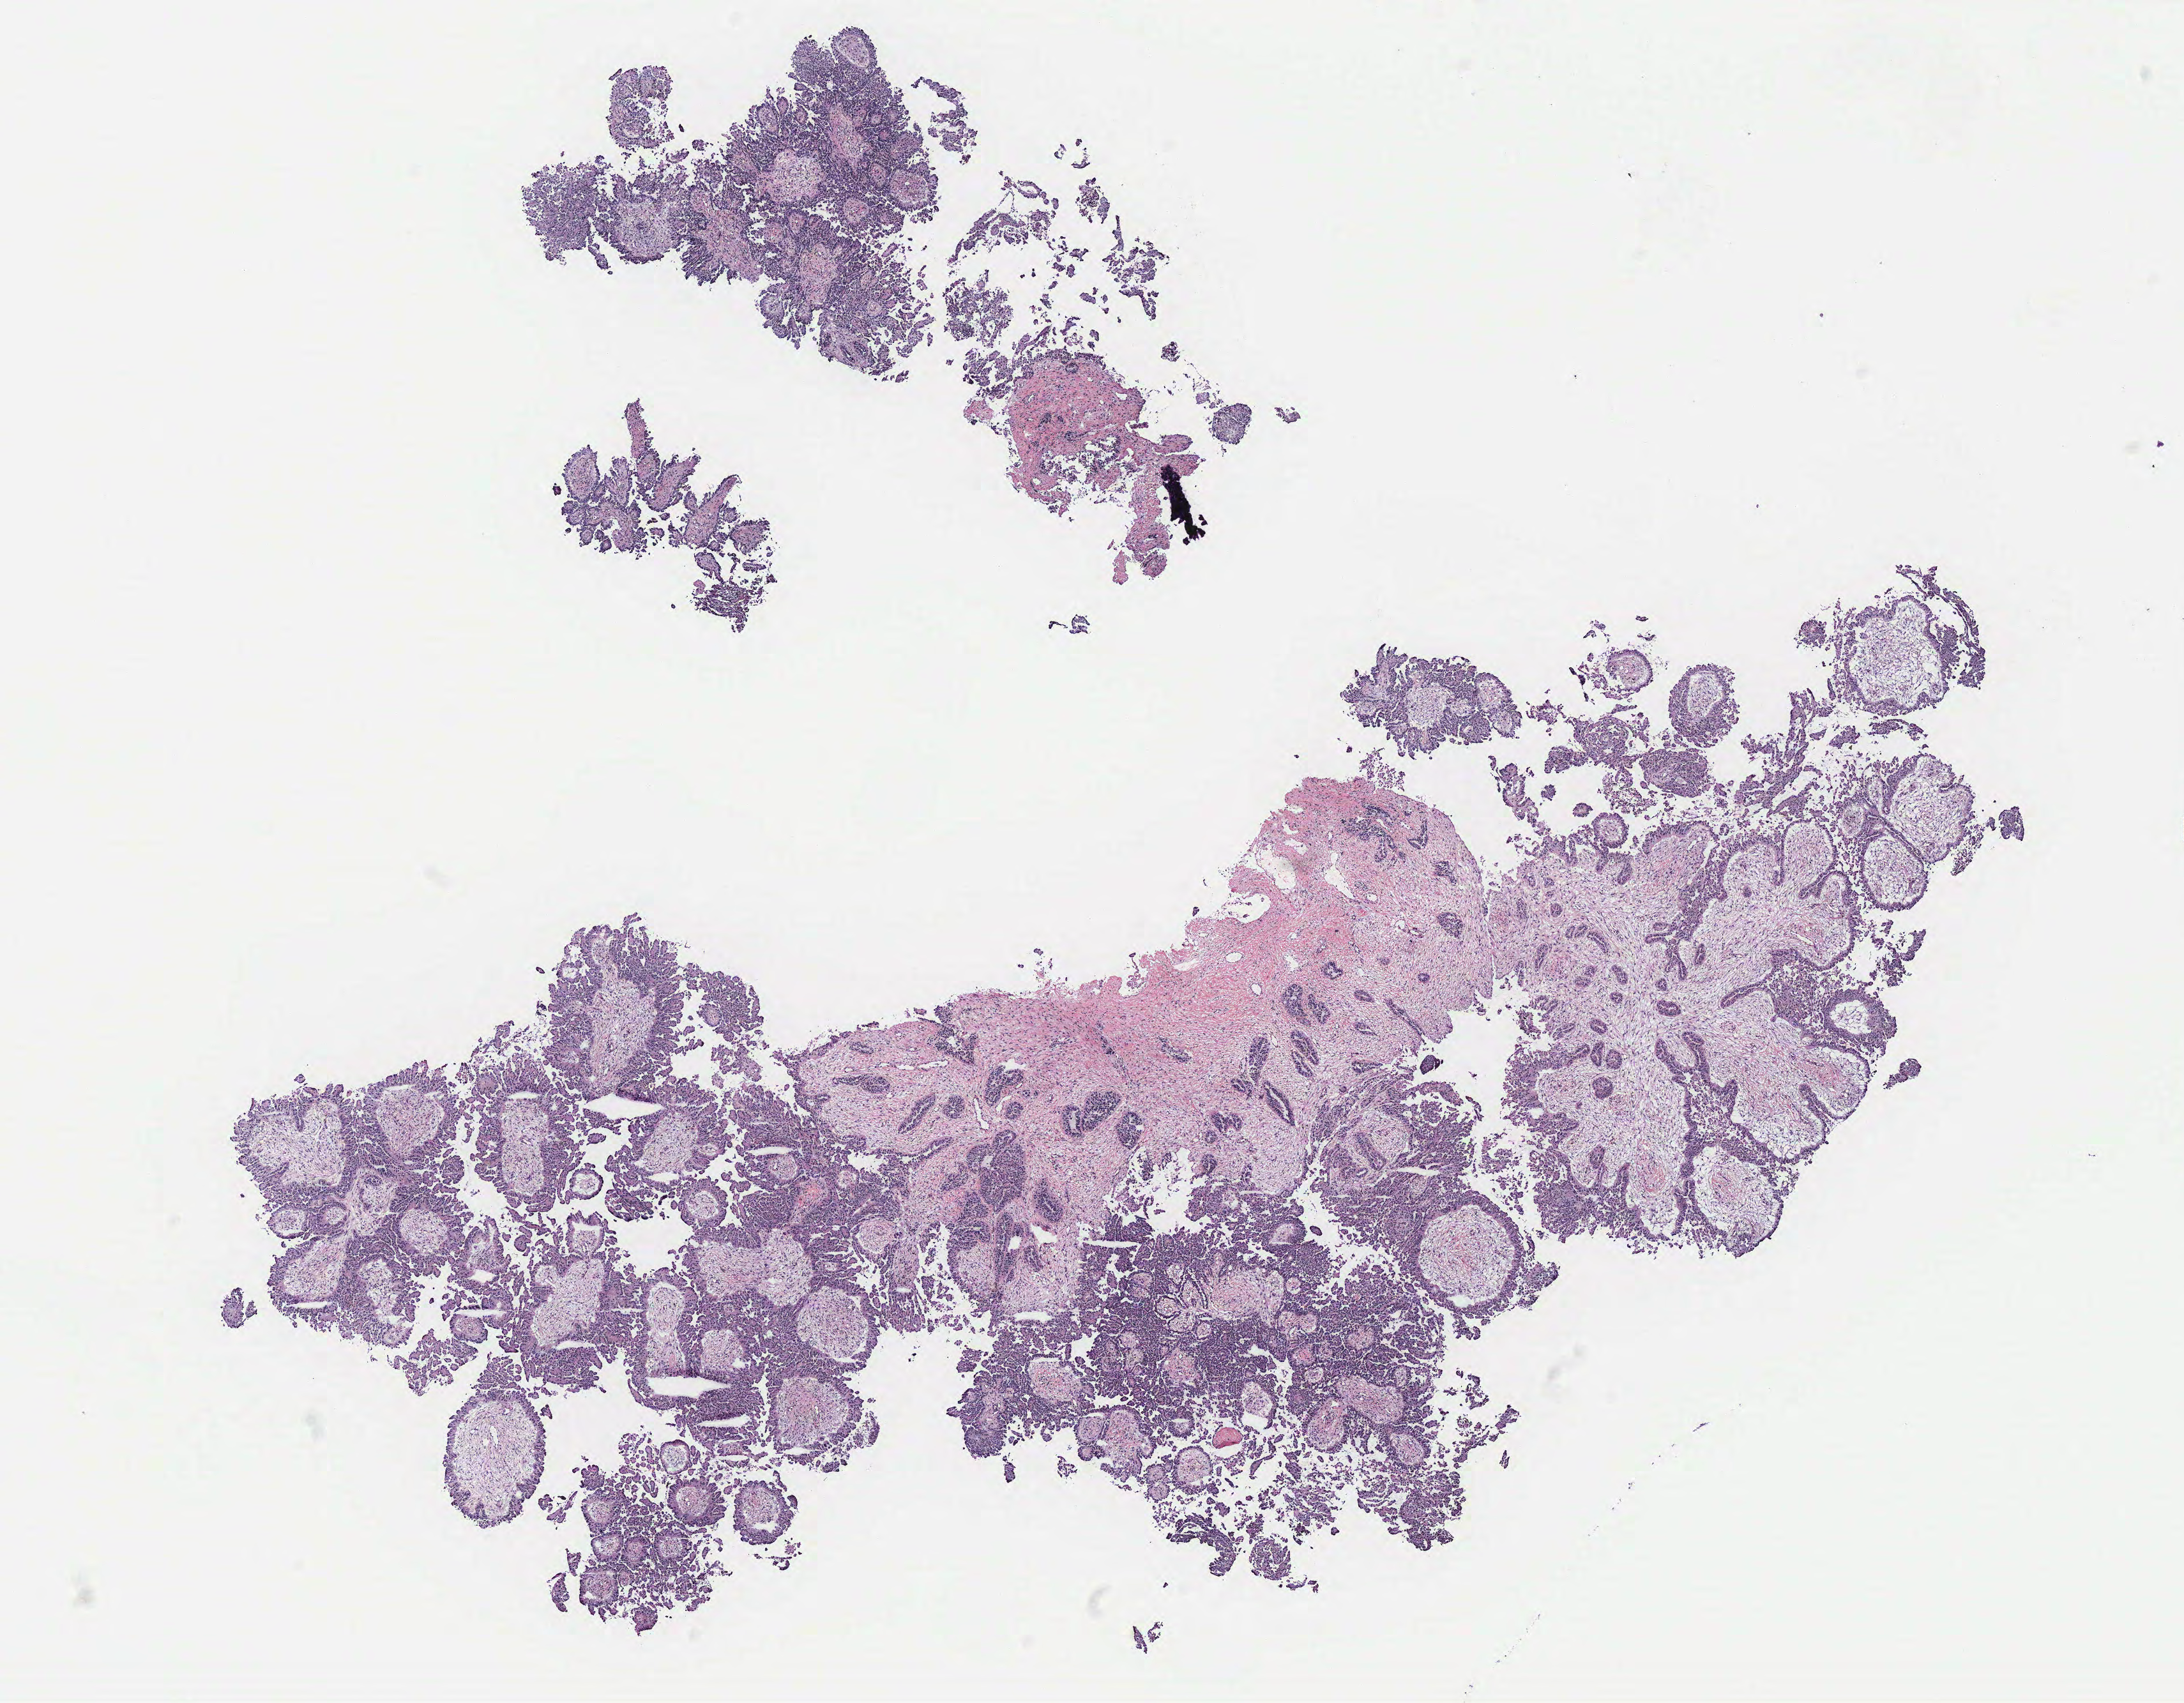
Digitized H&E-stained tissue section (whole slide), shown as a low-resolution overview of the whole scanned area (about 13.7 x 10.7 mm). Tumour tissue sample, ovary. 85-year-old female patient.
Histologic diagnosis: Serous adenocarcinoma, NOS.